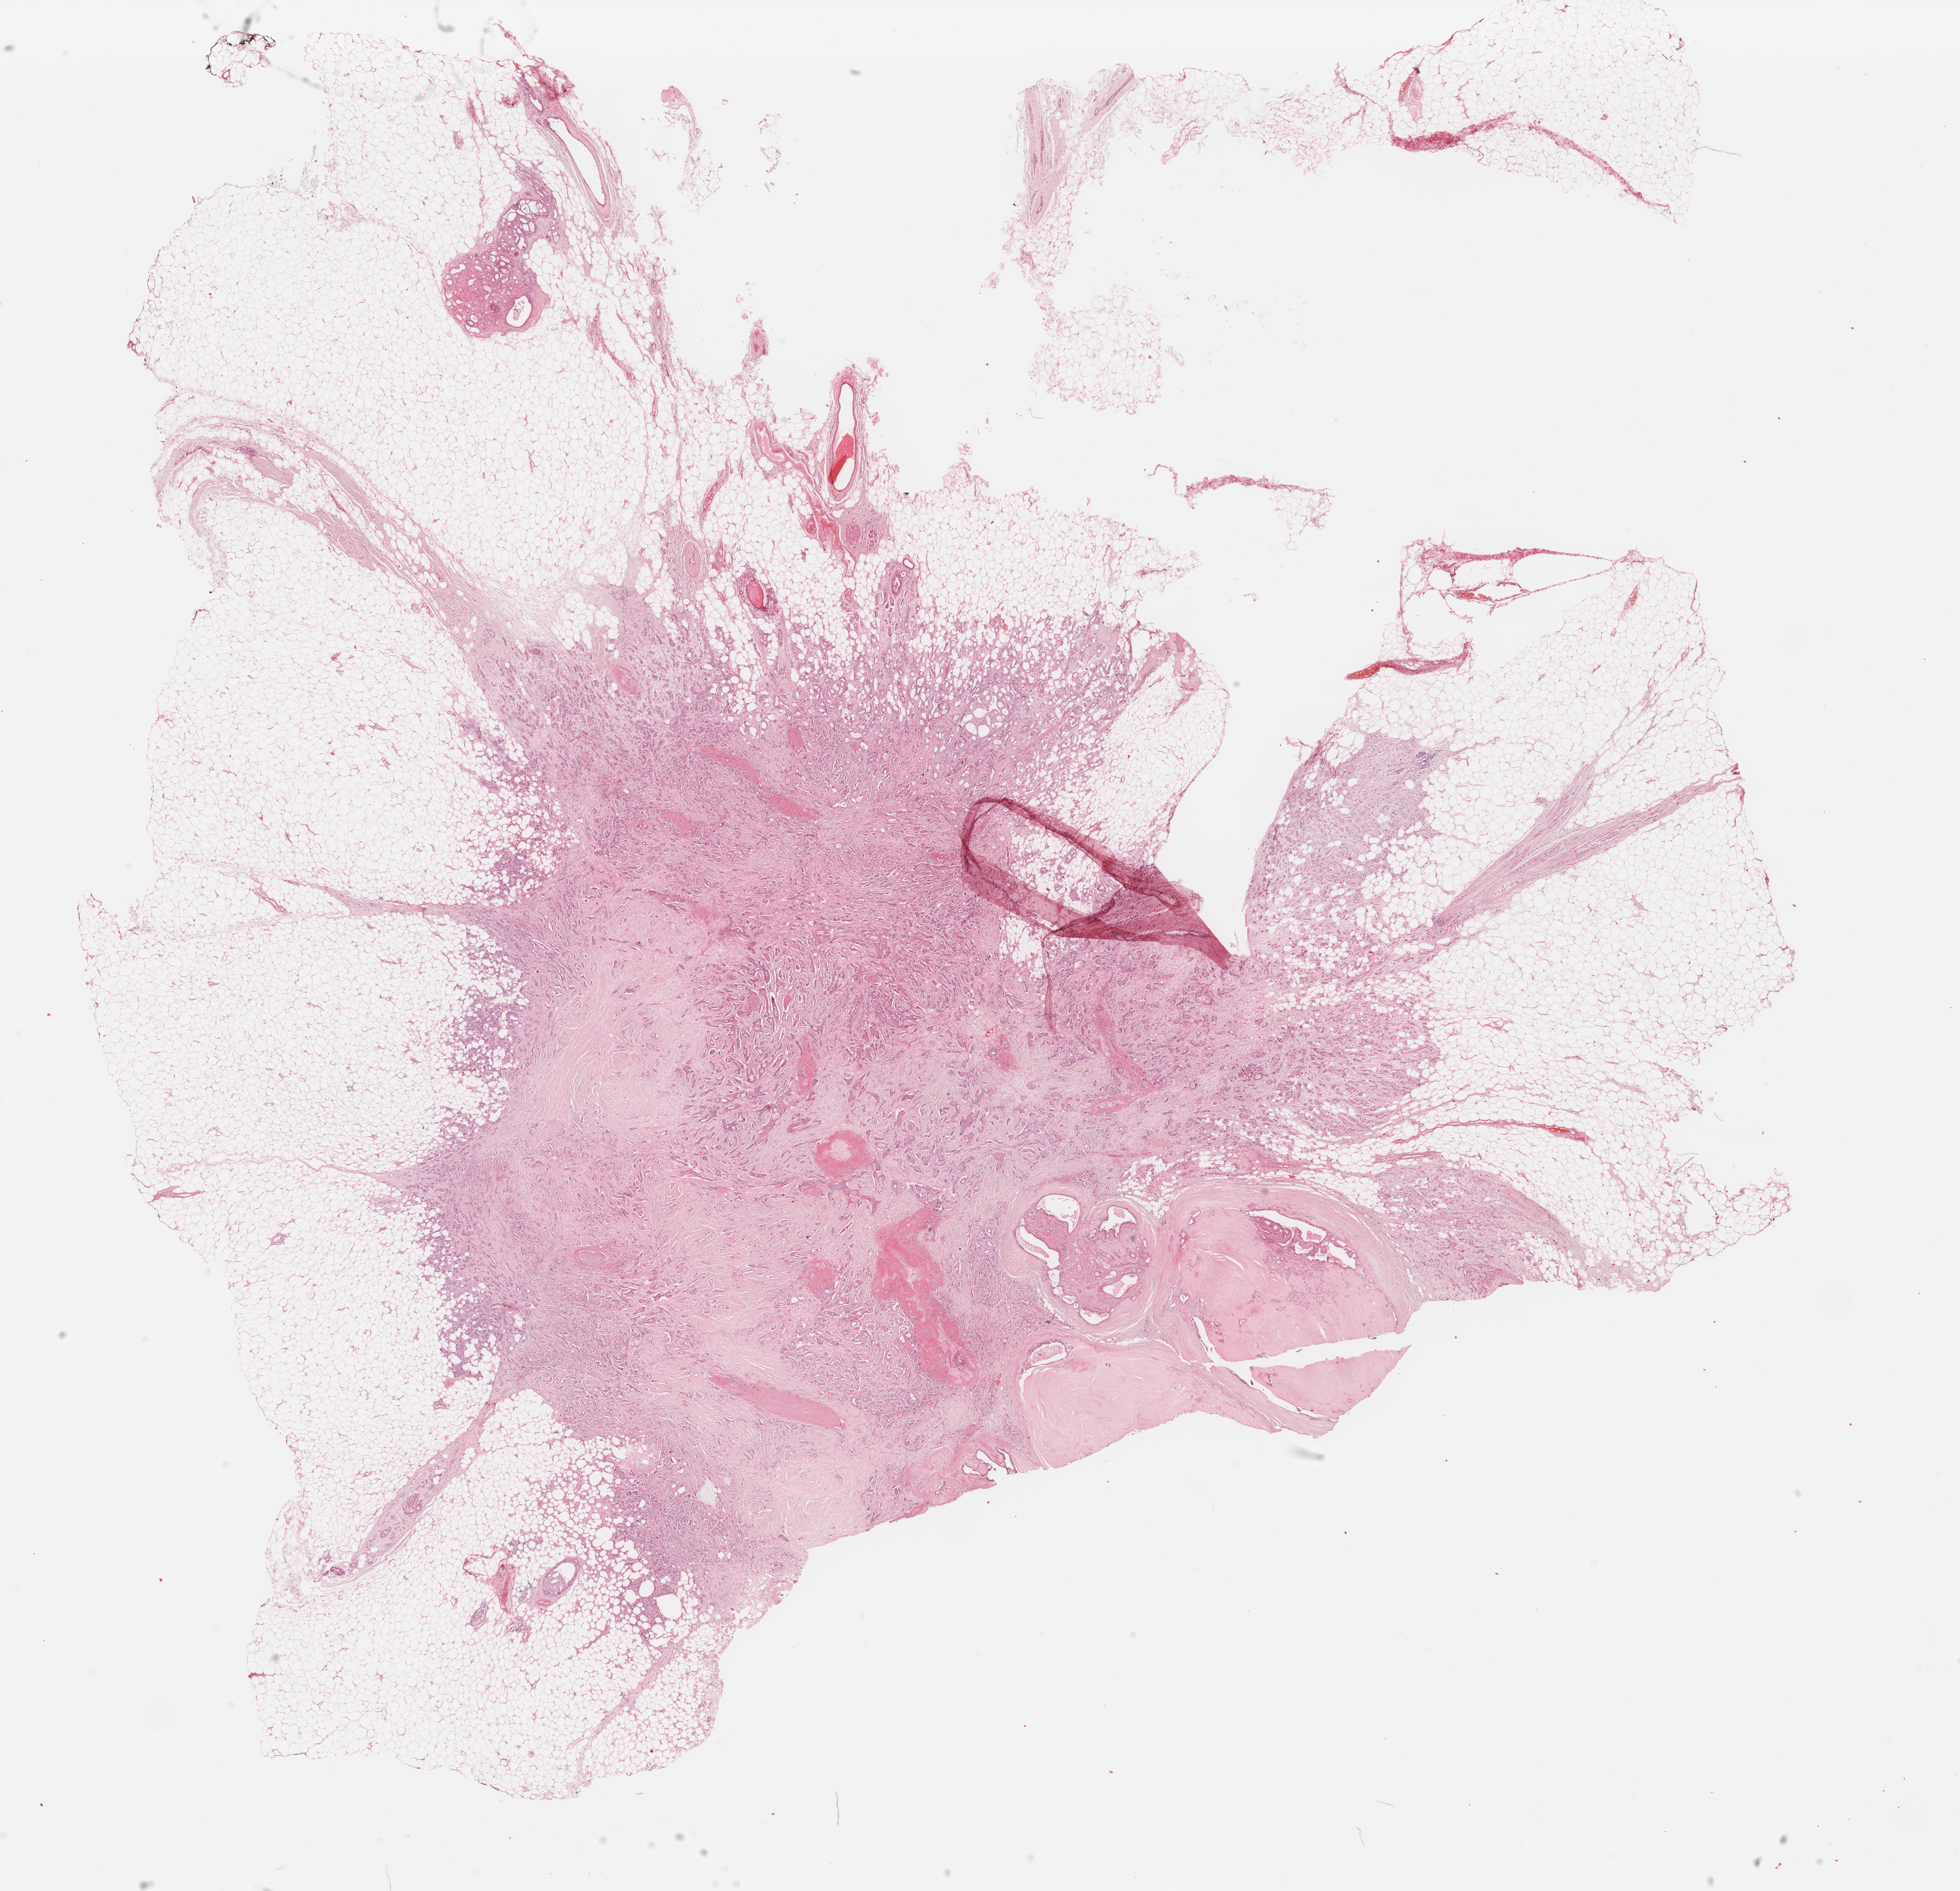
H&E-stained whole-slide image — shown as a low-resolution overview of the whole scanned area (about 22.9 x 22.1 mm), formalin-fixed paraffin-embedded (FFPE) diagnostic section, sample: primary tumour, breast. Patient: female, age at initial diagnosis 54 years.
AJCC pathologic stage: IIA. Pathologic diagnosis: Infiltrating duct carcinoma, NOS.